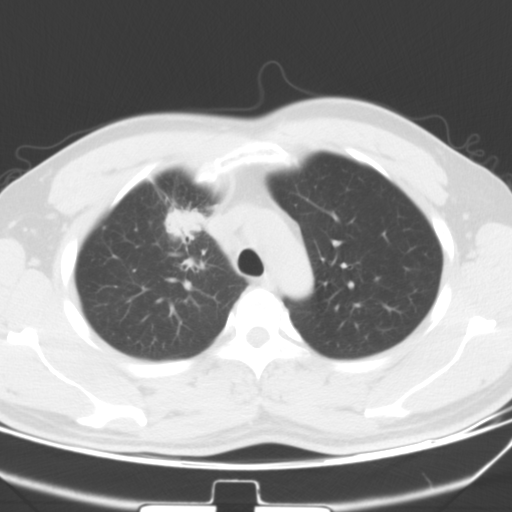
Chest CT, one axial slice; position 45 of 60 along the scan axis; lung window (W 1500 / L -600 HU); 5 mm slice thickness; 512 × 512 image matrix, field of view 337 × 337 mm. Male patient, age 35 years. Case-level facts recorded for this patient, not image findings: clinical TNM (as recorded): T1c N1 M1b.
Structures marked on this image (rectangle marked by the reading radiologist):
- lung tumour (recorded histology: adenocarcinoma): bounding box (x1, y1, x2, y2) in pixels: (166, 209, 207, 238)